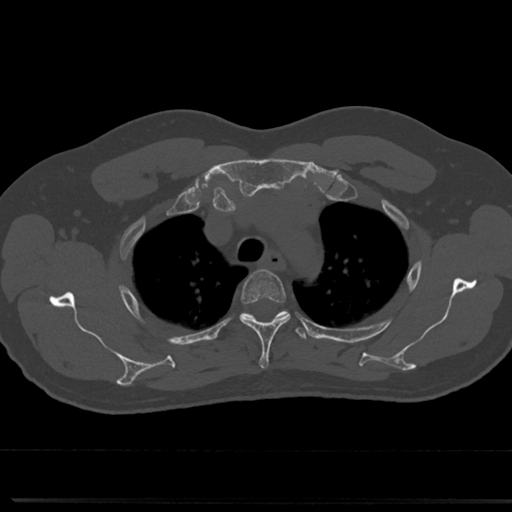
CT including the spine, one axial slice. Slice 580 of 817 in the series (ordered by position). 120 kVp. Bone window (W 1800 / L 400 HU). 0.5 mm slice thickness. 512 × 512 image matrix. Patient: male, 61 years. From the clinical record (not read from this slice): primary cancer: prostate.
Outlined on this slice (semi-automatically segmented with operator editing):
- T3 vertebra: box from (x=239, y=270) to (x=290, y=369) px
- T4 vertebra: (x=222, y=309)–(x=309, y=343)